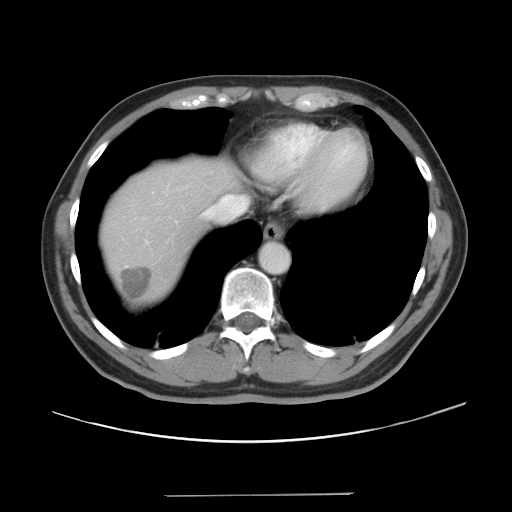
Contrast-enhanced abdominal CT, one axial slice. Position 36 of 43 along the scan axis. Intravenous contrast given. Soft-tissue window (W 400 / L 40 HU). 5 mm slice thickness. 512 × 512 image matrix. Male patient, age 65 years. From the clinical record (not read from this slice): diagnosis: colorectal cancer liver metastases, imaged before liver resection; multiple liver metastases: no; largest metastasis: 3.8 cm; disease in both lobes: no.
Outlined on this slice (expert manual segmentation):
- hepatic veins: bounding box (x1, y1, x2, y2) in pixels: (204, 199, 223, 217)
- liver: (102, 162, 243, 303)
- planned liver remnant (the part of the liver to remain after resection): (103, 162, 244, 276)
- liver metastasis: (119, 267, 151, 299)